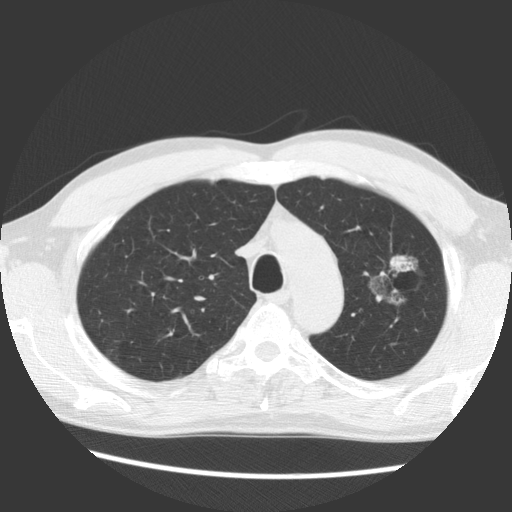
Chest CT (low-dose screening protocol), one axial image. First (baseline) screen. Lung window (W 1500 / L -600 HU). 2.5 mm slice thickness. Slice 104 of 138 in the series. 512 × 512 image matrix, field of view 340 × 340 mm. Male participant, aged 61 years at enrolment. Former smoker at enrolment.
Expert-annotated lung lesion, bounding box (x1, y1, x2, y2) in pixels: (352, 242, 437, 321). Reader record for this screening exam (exam-level; its link to the box is not recorded): non-calcified nodule or mass ≥4 mm, left upper lobe, 17 × 14 mm, soft tissue attenuation. Official screen result: positive, change unspecified: nodule(s) >= 4 mm or enlarging nodule(s), mass(es), or other non-specific abnormalities suspicious for lung cancer. Later outcome: lung cancer diagnosed 1061 days after this screen — bronchiolo-alveolar adenocarcinoma, NOS, left upper lobe, well differentiated (G1), stage IB (AJCC 6th edition), 44 mm at pathology.